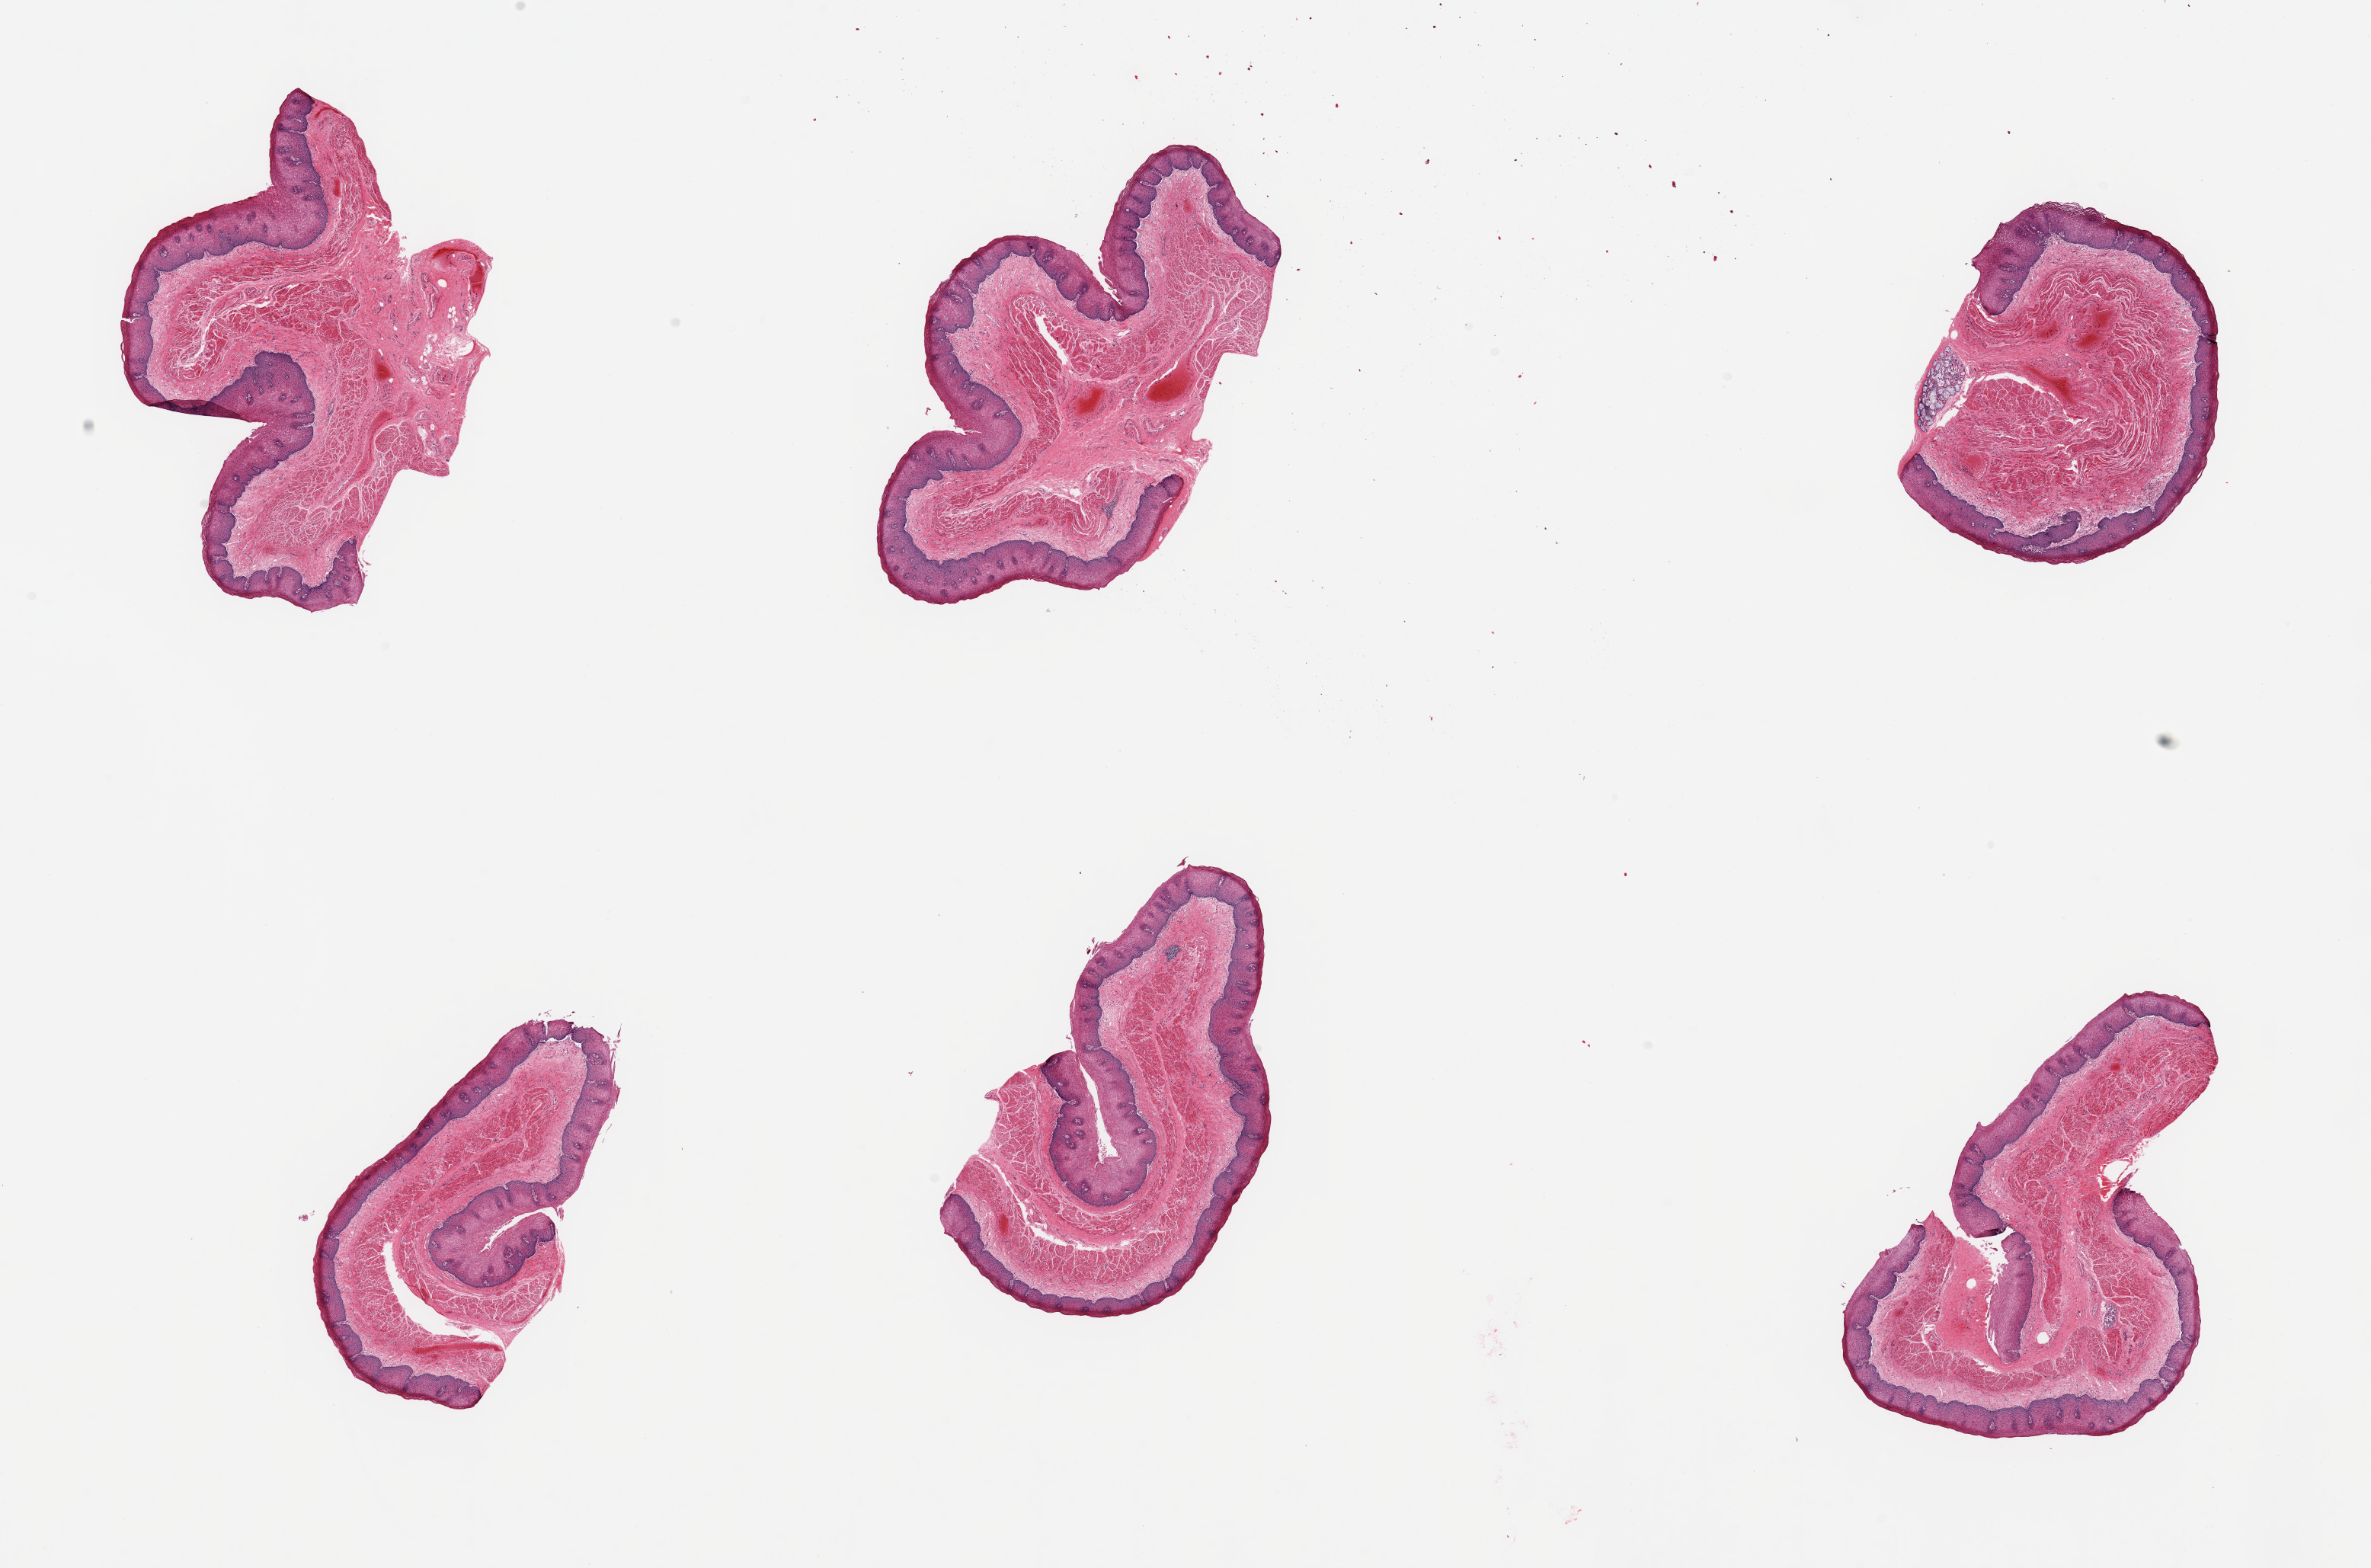
H&E whole-slide image, brightfield — shown as a low-resolution overview of the whole scanned area (about 24.6 x 16.3 mm, acquisition: 20x scan), PAXgene-fixed paraffin-embedded (PFPE) section, sampled site (target tissue): esophageal mucous membrane, tissue donor sample. Male donor.
Pathologist's review note for this sample: 6 pieces; well preserved; 1 small [0.8mm] submucosal gland on 1 deep edge.